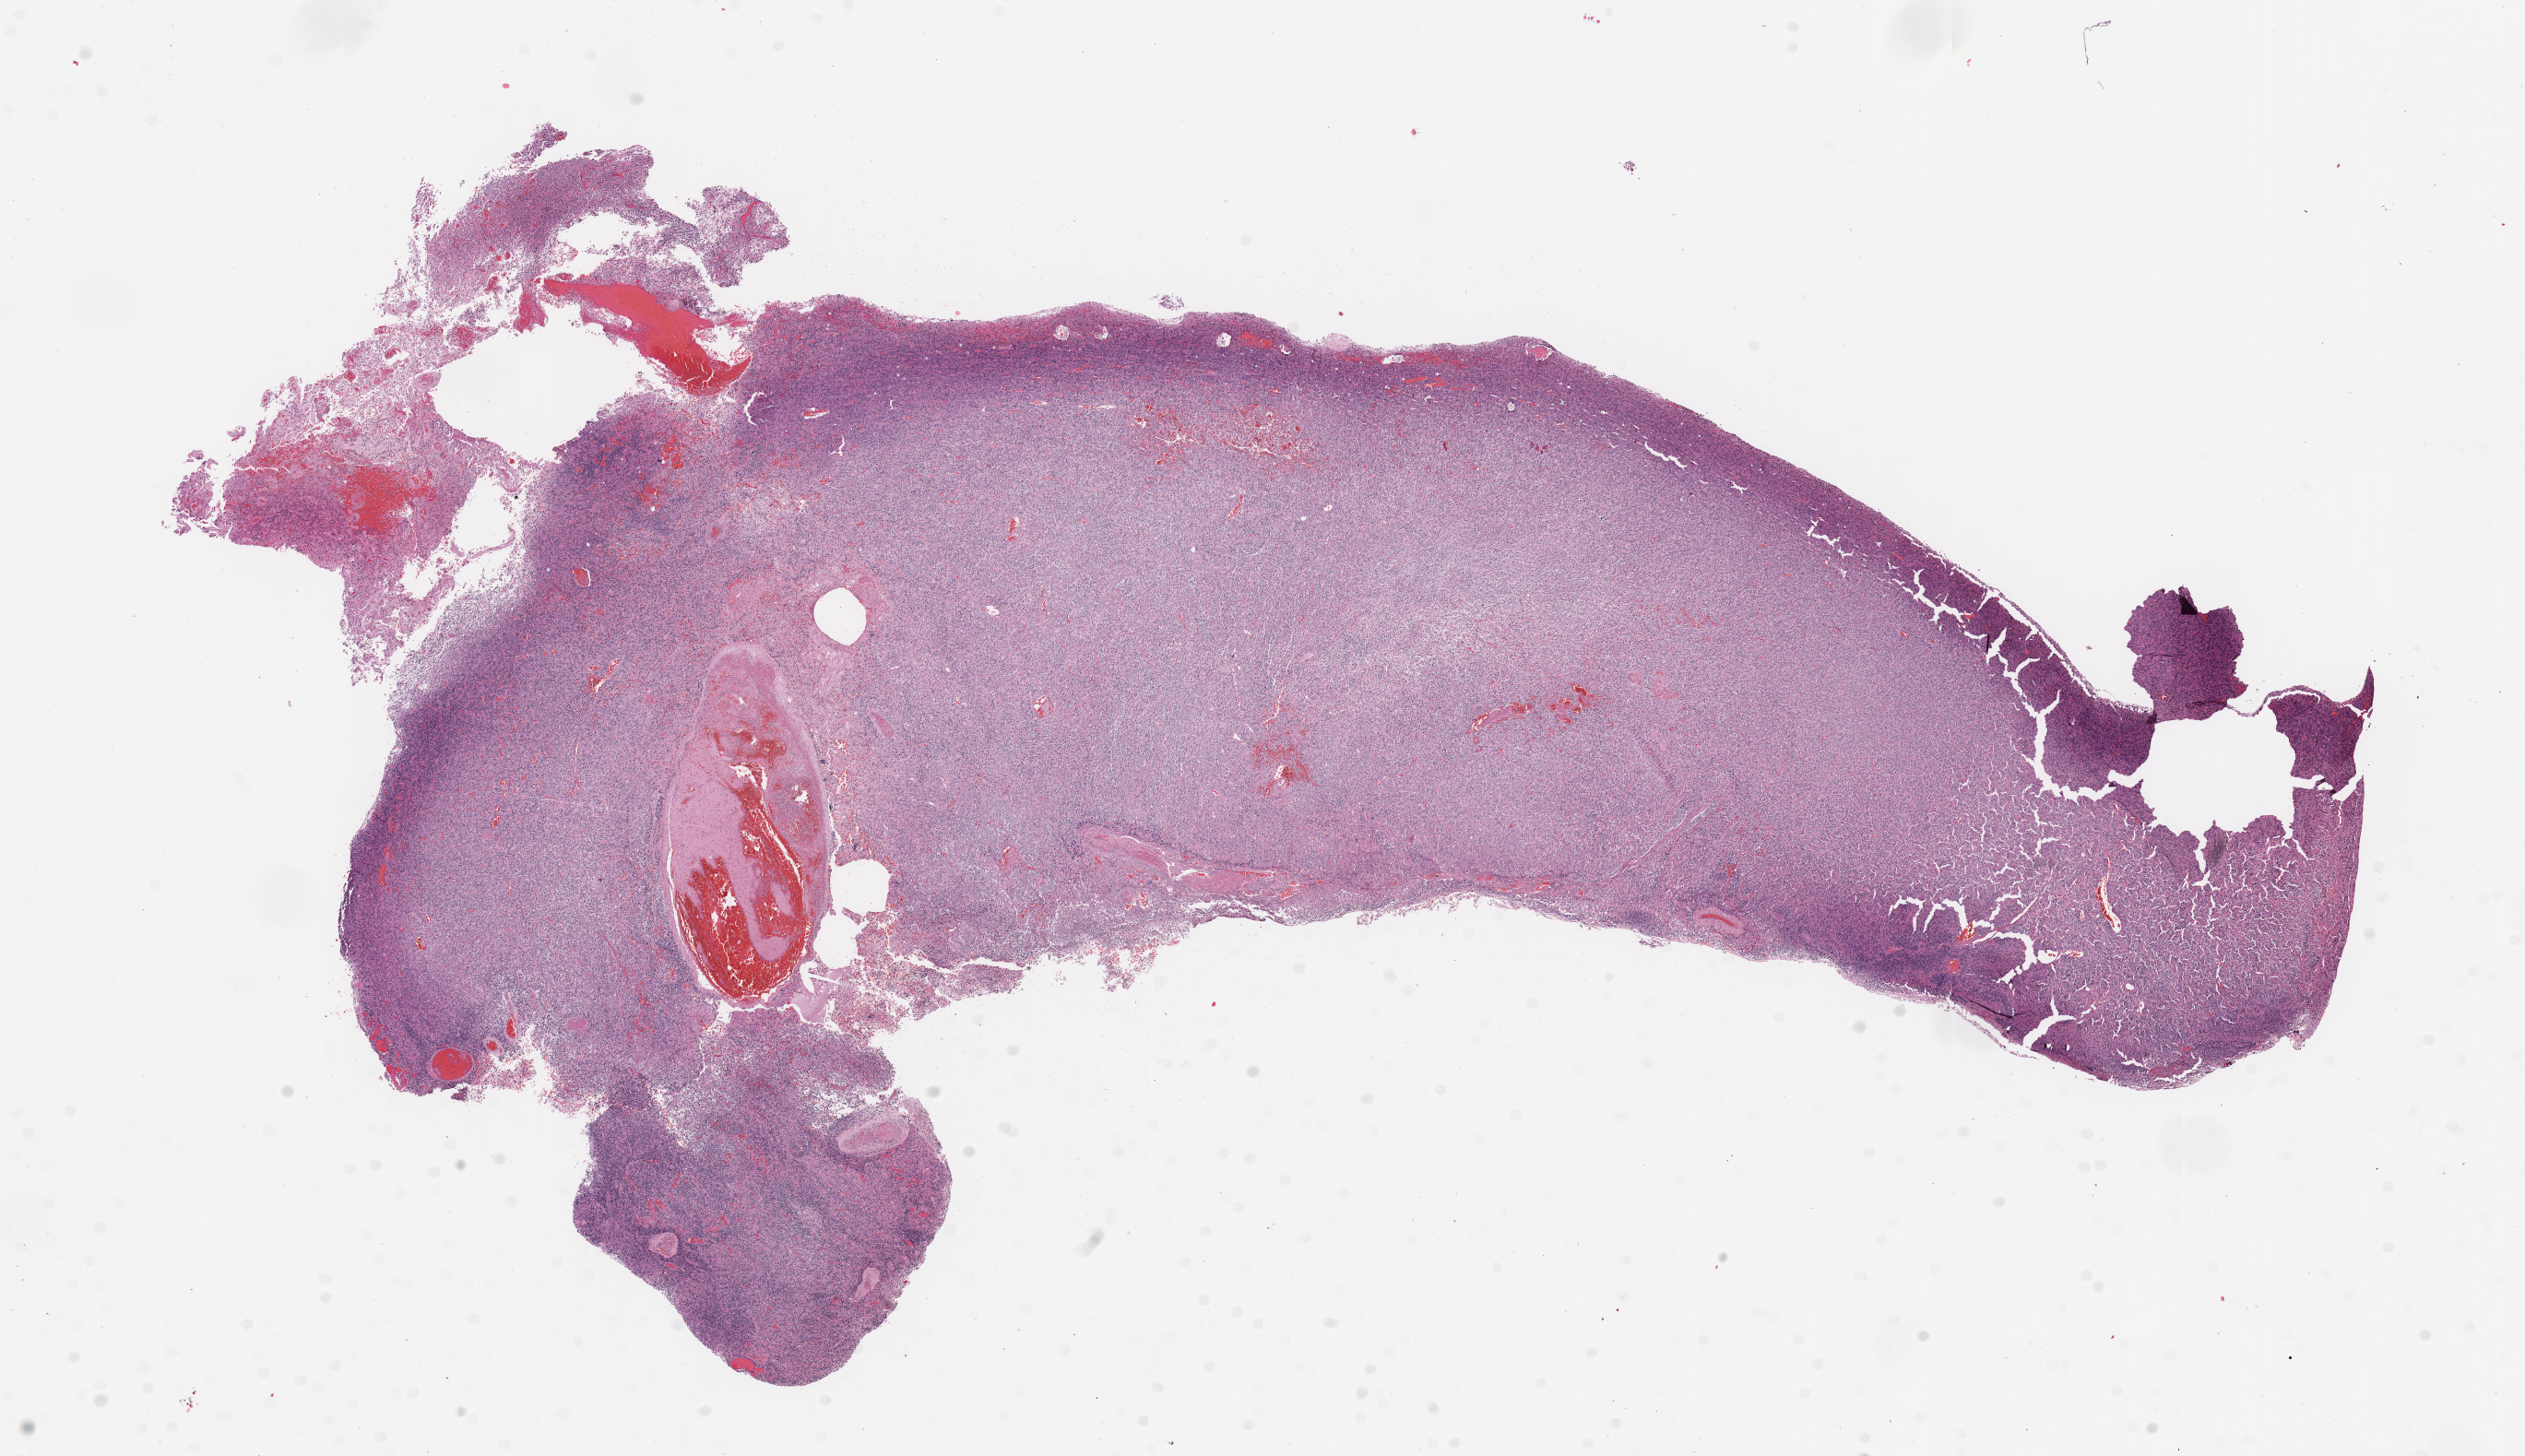
Digitized Hematoxylin and eosin (H&E) stained tissue section (whole slide) — whole scanned area (about 21.7 x 12.5 mm, from a 20x scan) shown as a low-resolution overview, tumour tissue sample, sampled site: brain. Patient: male, age 70 years. Pathologist review of this section (percent, as recorded): tumour nuclei 80%, necrosis 5%.
Primary tumour site (as recorded): parietal lobe. Histologic diagnosis: Glioblastoma.